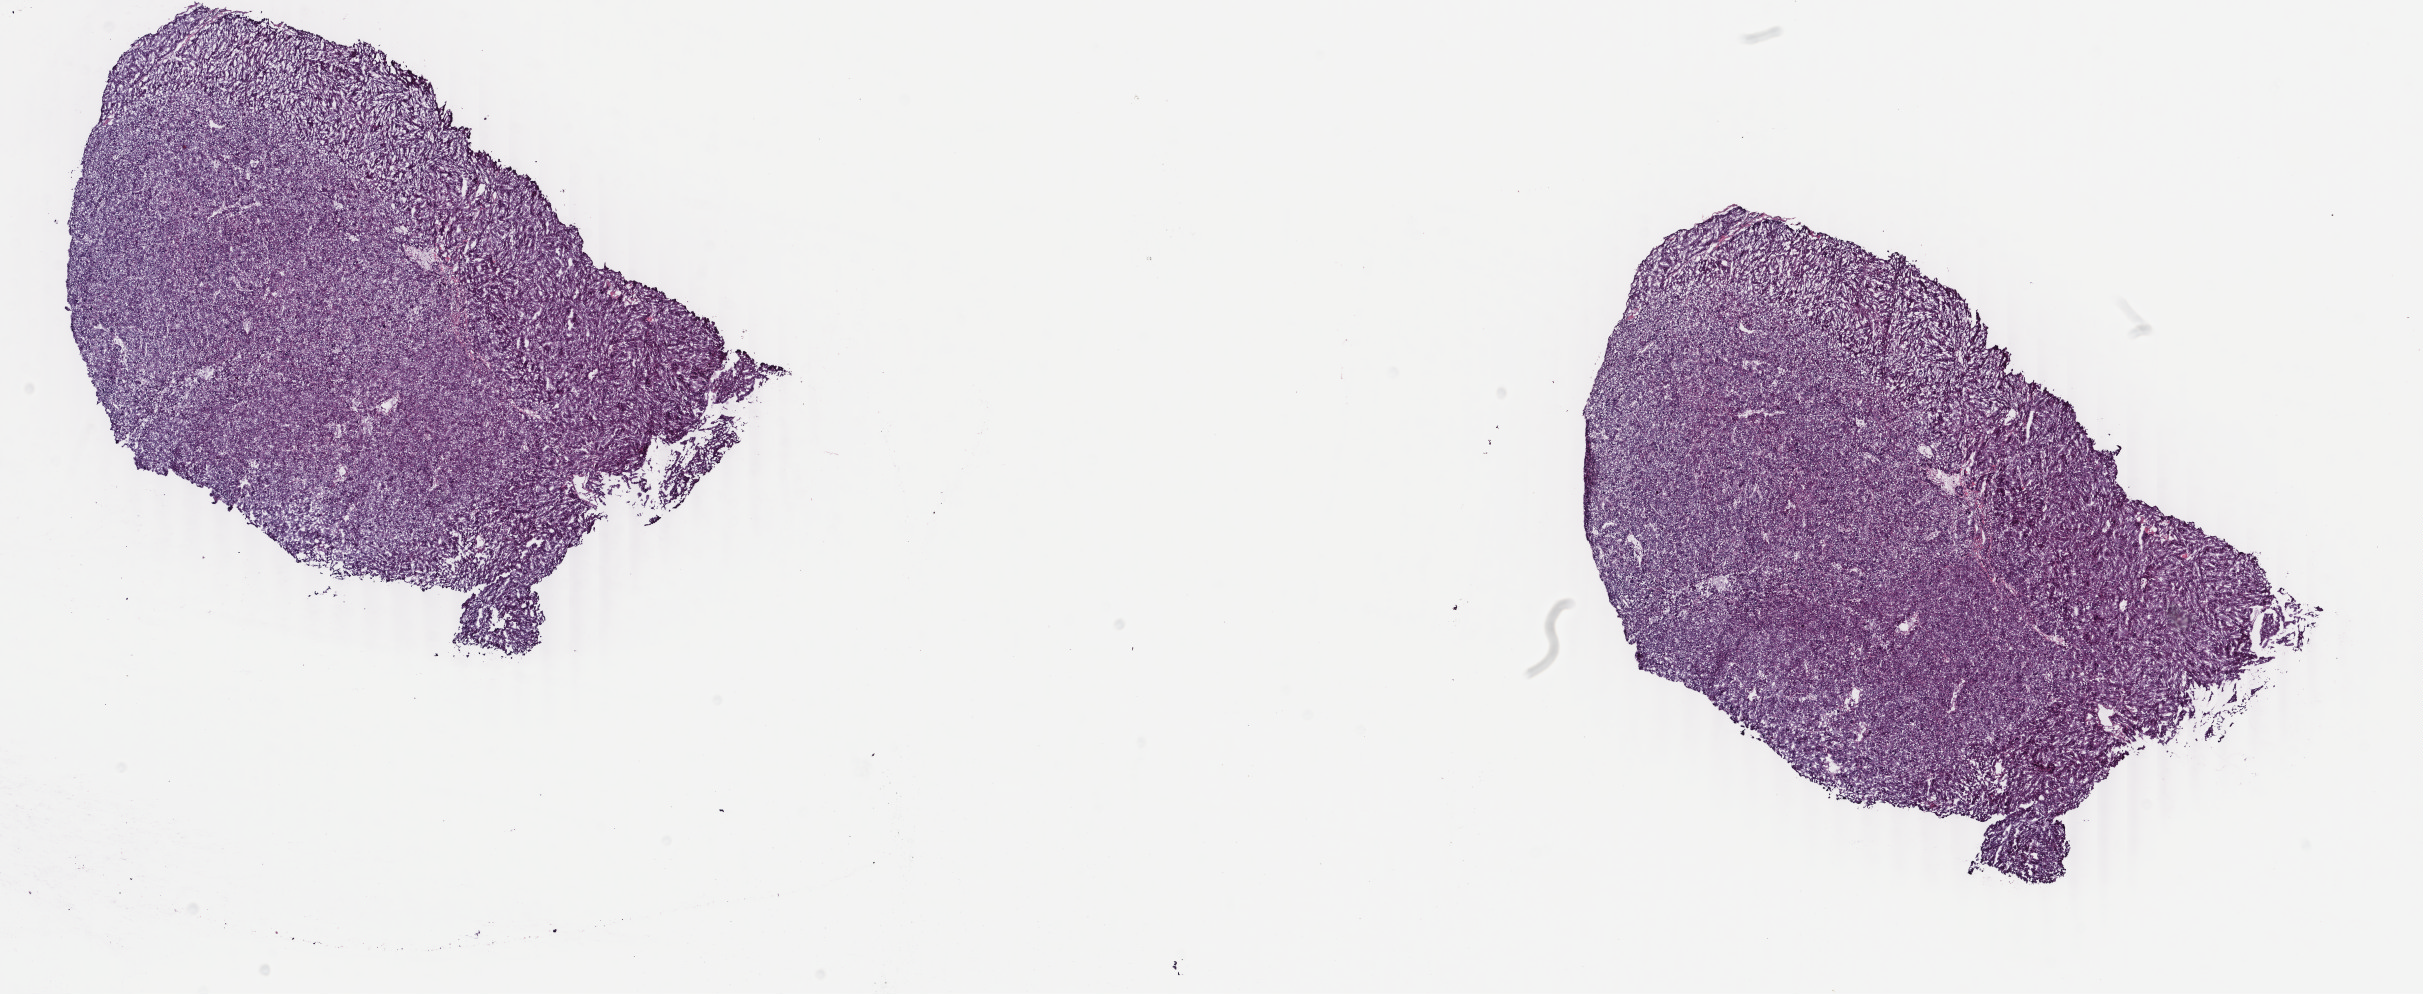
H&E whole-slide image, low-resolution overview of the scanned area, about 19.3 x 7.9 mm (slide scanned at 40x); frozen section from the bottom of the tissue portion; liver, primary tumour sample. Female, age 55 years at initial diagnosis.
Pathologic diagnosis: Hepatocellular carcinoma, NOS.